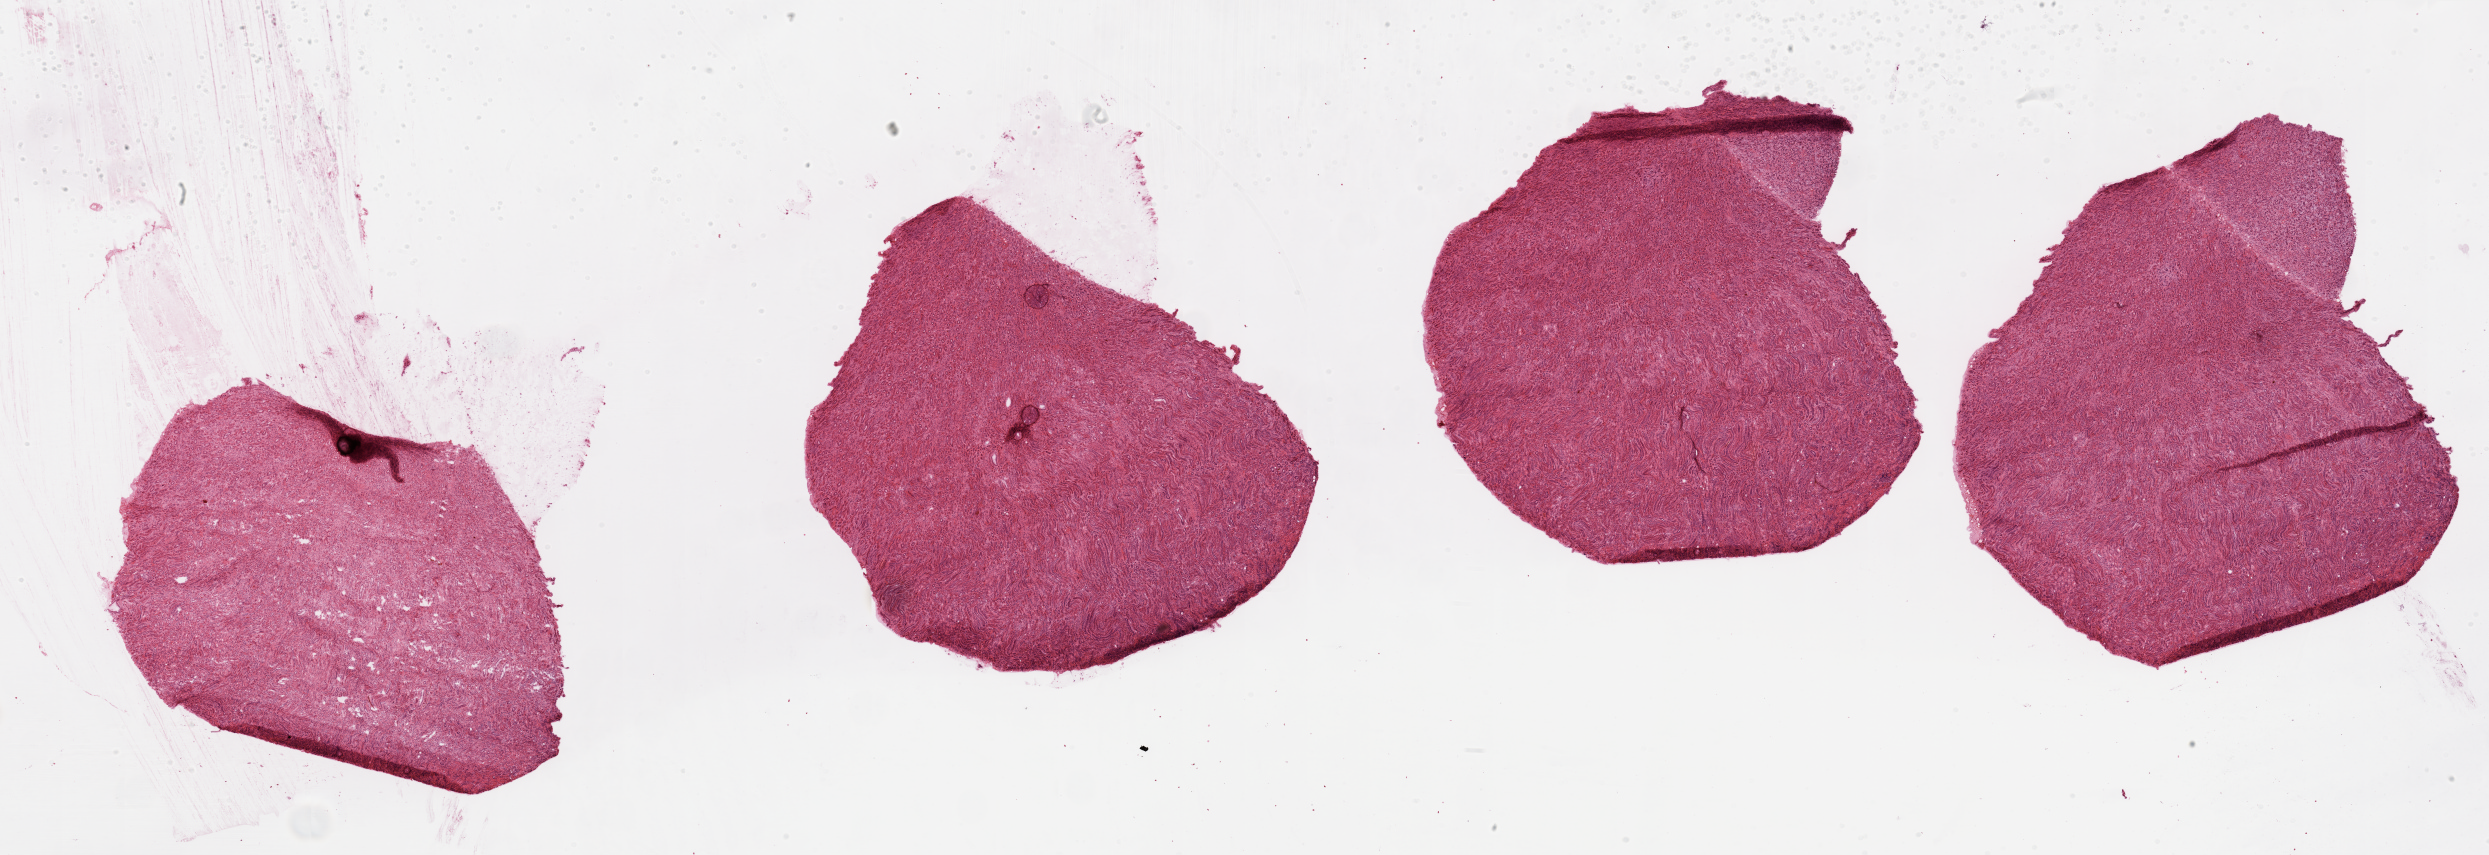
Digitized Hematoxylin and eosin (H&E) stained tissue section (whole slide) — shown as a low-resolution overview of the whole scanned area (about 39.4 x 13.5 mm, from a 20x scan). Normal (non-tumour) tissue sample, sampled site: kidney. 54-year-old male patient.
This section: normal (non-tumour) tissue from the same patient. Patient diagnosis: Renal cell carcinoma, NOS.